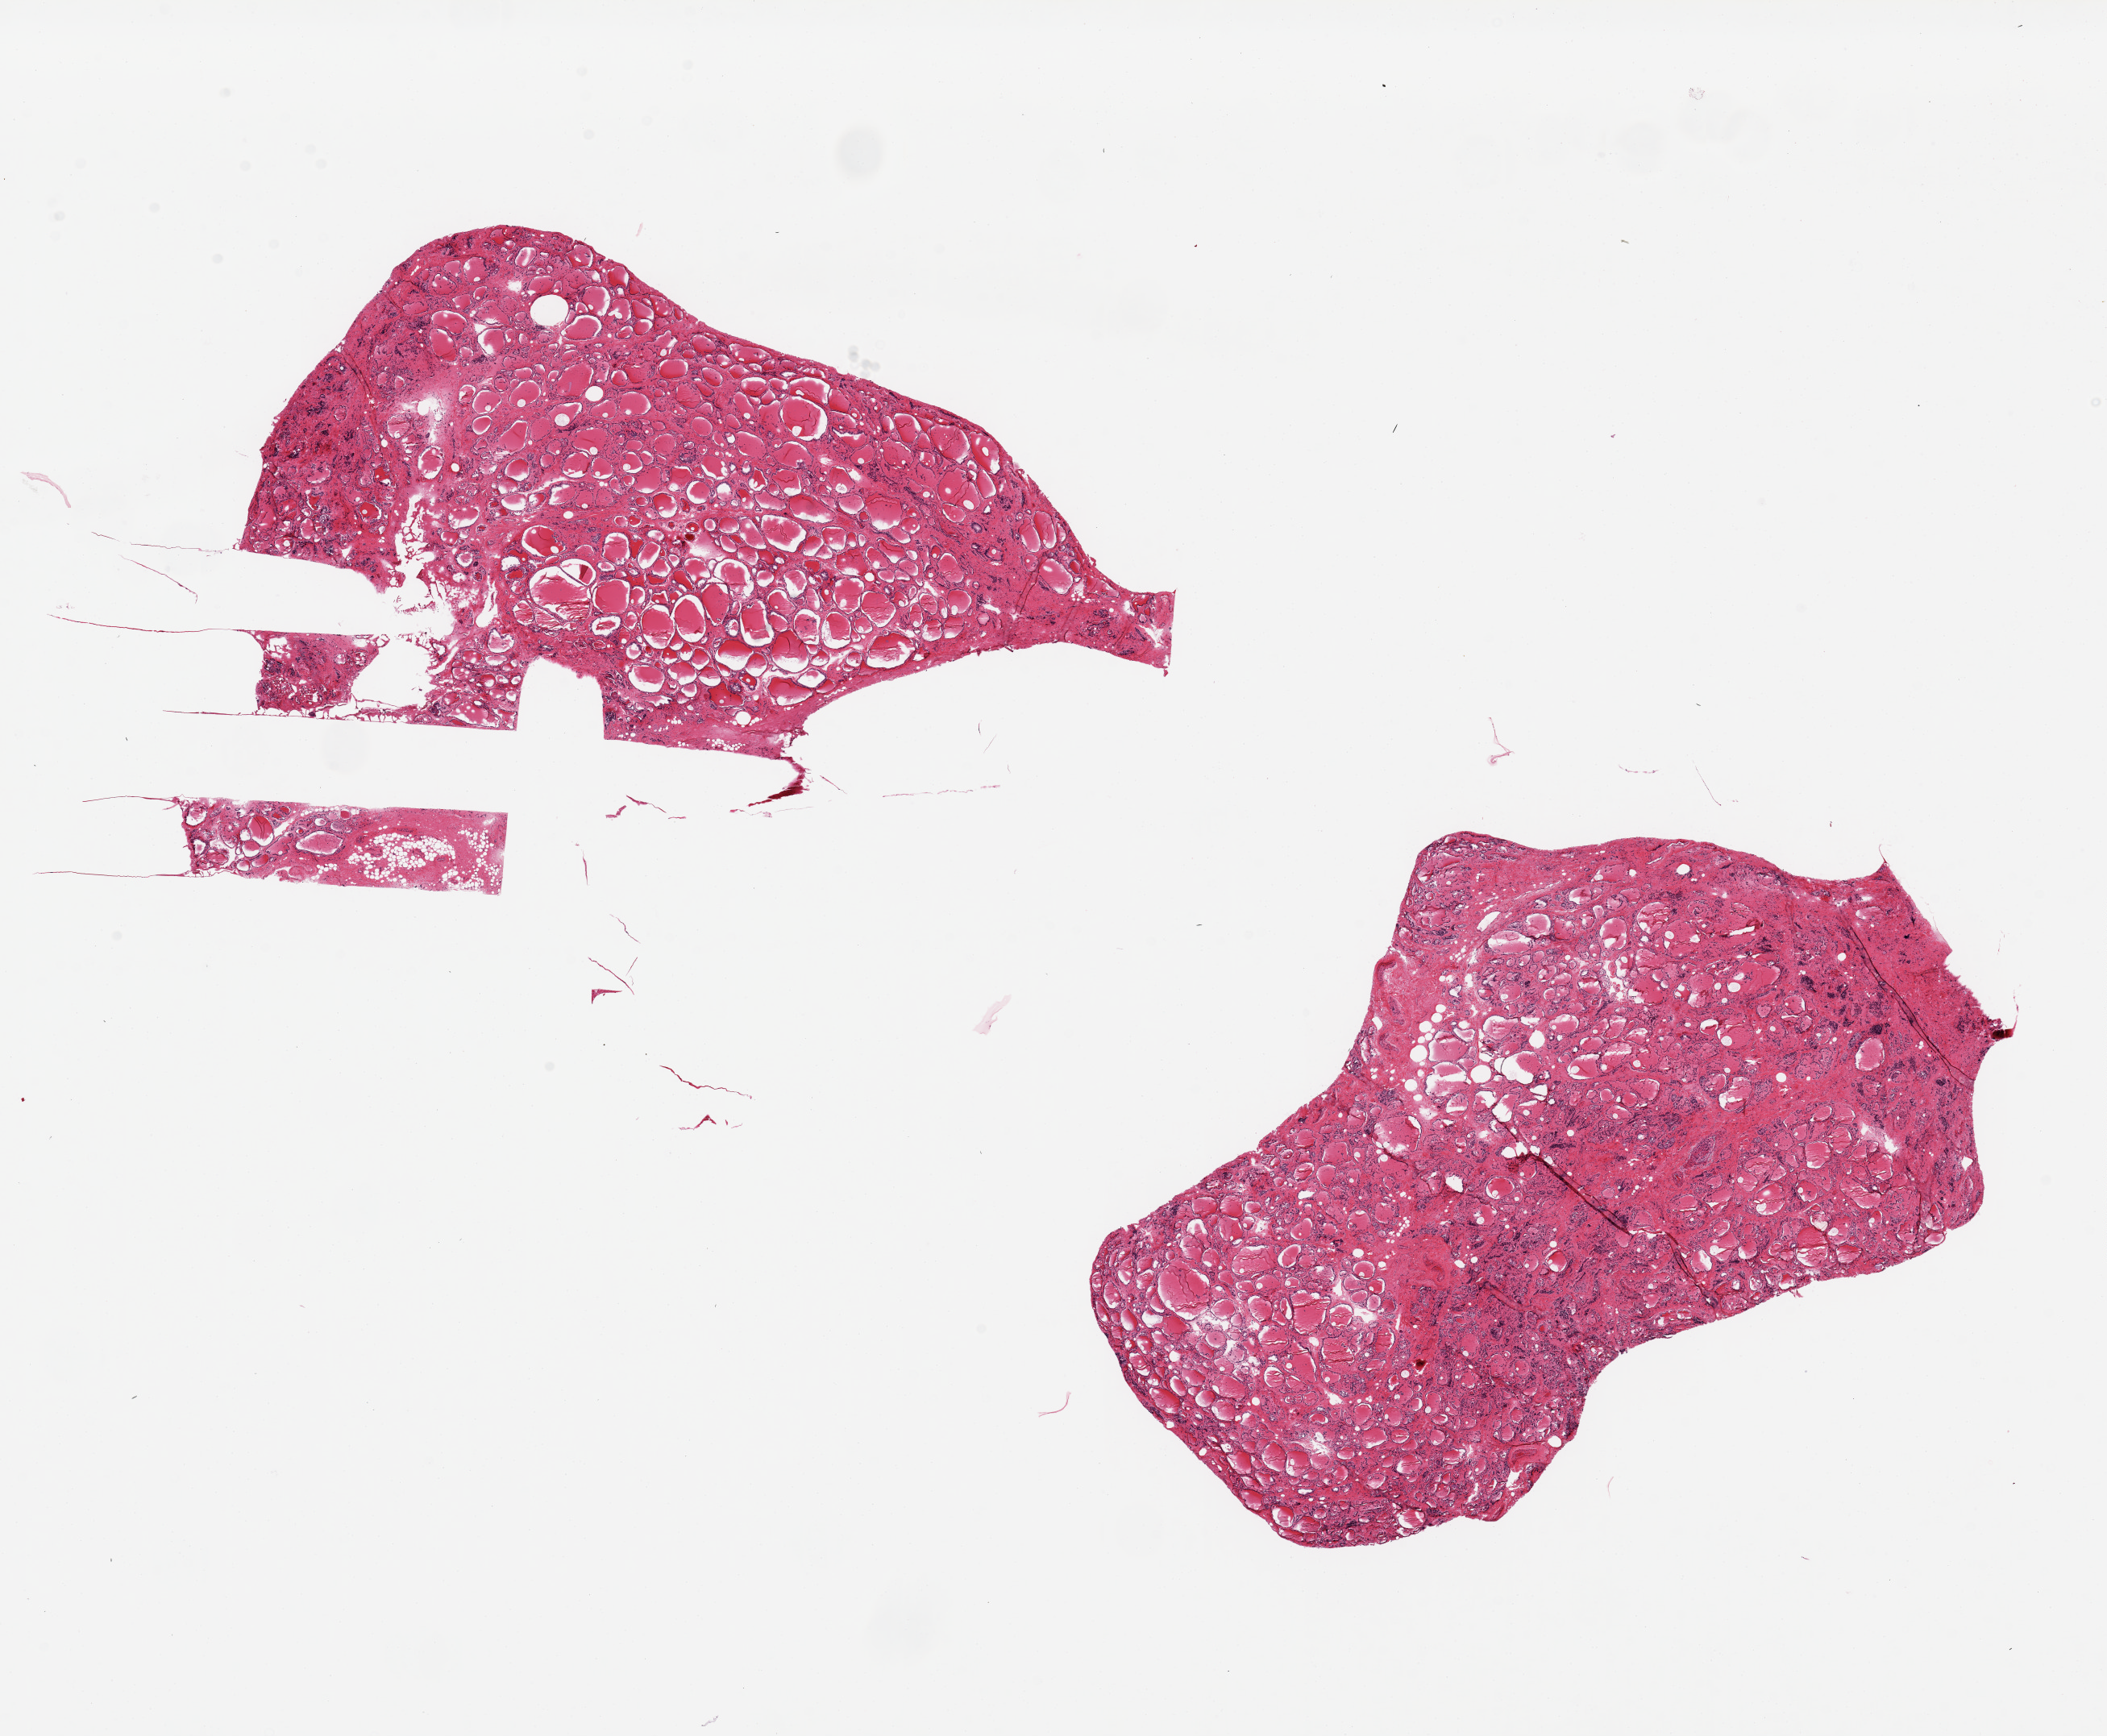
Digitized H&E-stained section, brightfield — shown as a low-resolution overview of the whole scanned area (about 20.7 x 17.0 mm, acquisition: 20x scan); PAXgene-fixed, paraffin-embedded tissue; section of thyroid (target tissue); donor tissue sample. Donor: male.
• reviewer comment on this tissue sample: 2 pieces, 11x9 & 9x6mm